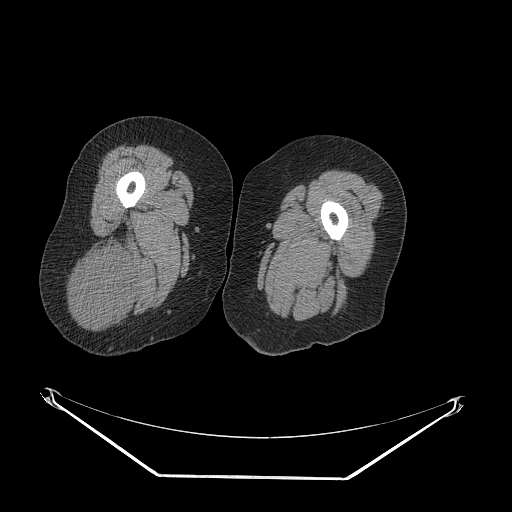
CT of an extremity soft-tissue mass (from a PET/CT study), one axial slice; slice 32 of 257 in the series (ordered by position); soft-tissue window (W 400 / L 40 HU); 512 × 512 image matrix, field of view 500 × 500 mm. Female patient. Case-level facts recorded for this patient, not image findings: histological type: synovial sarcoma; grade: intermediate; site of the primary tumour: right buttock.
Outlined on this slice (expert contour drawn on MRI and transferred to this co-registered scan by the dataset authors):
- gross tumour volume including surrounding oedema: box from (x=69, y=242) to (x=136, y=327) px
- gross tumour volume (mass): (x=73, y=247)–(x=136, y=327)